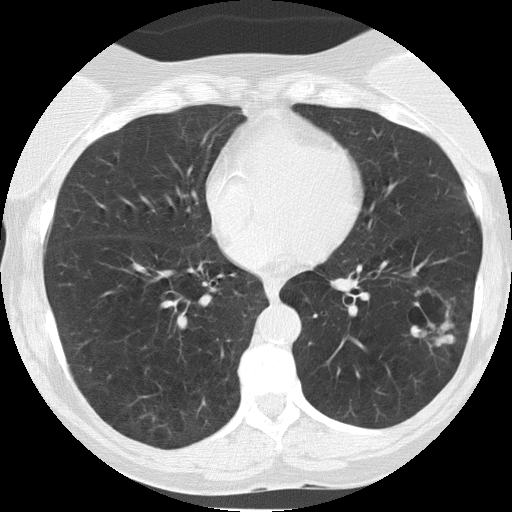
Low-dose screening chest CT, one axial slice; slice 65 of 149 in the series (ordered by position); reconstruction kernel FC51; lung window (W 1500 / L -600 HU); 2 mm slice thickness; 512 × 512 image matrix.
Outlined on this slice (expert manual segmentation):
- lesion 1 (tumor, lower lobe of left lung): bounding box <411,321,454,346> (left, top, right, bottom; pixels)